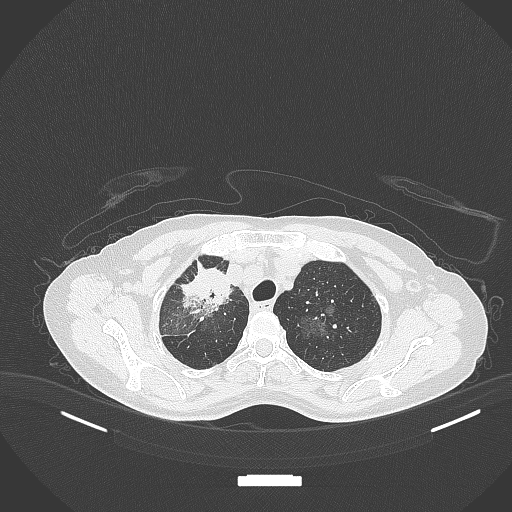
Chest CT, one axial slice; slice 267 of 284 in the series (ordered by position); reconstruction kernel B70f; lung window (W 1500 / L -600 HU); 1 mm slice thickness; 512 × 512 image matrix, field of view 400 × 400 mm. Patient: female, 59 years. From the clinical record (not read from this slice): clinical TNM (as recorded): T3 N0 M0; histopathological grade: G1.
Structures marked on this image (bounding box drawn by a radiologist):
- lung tumour (recorded histology: adenocarcinoma): box from (x=177, y=266) to (x=234, y=321) px